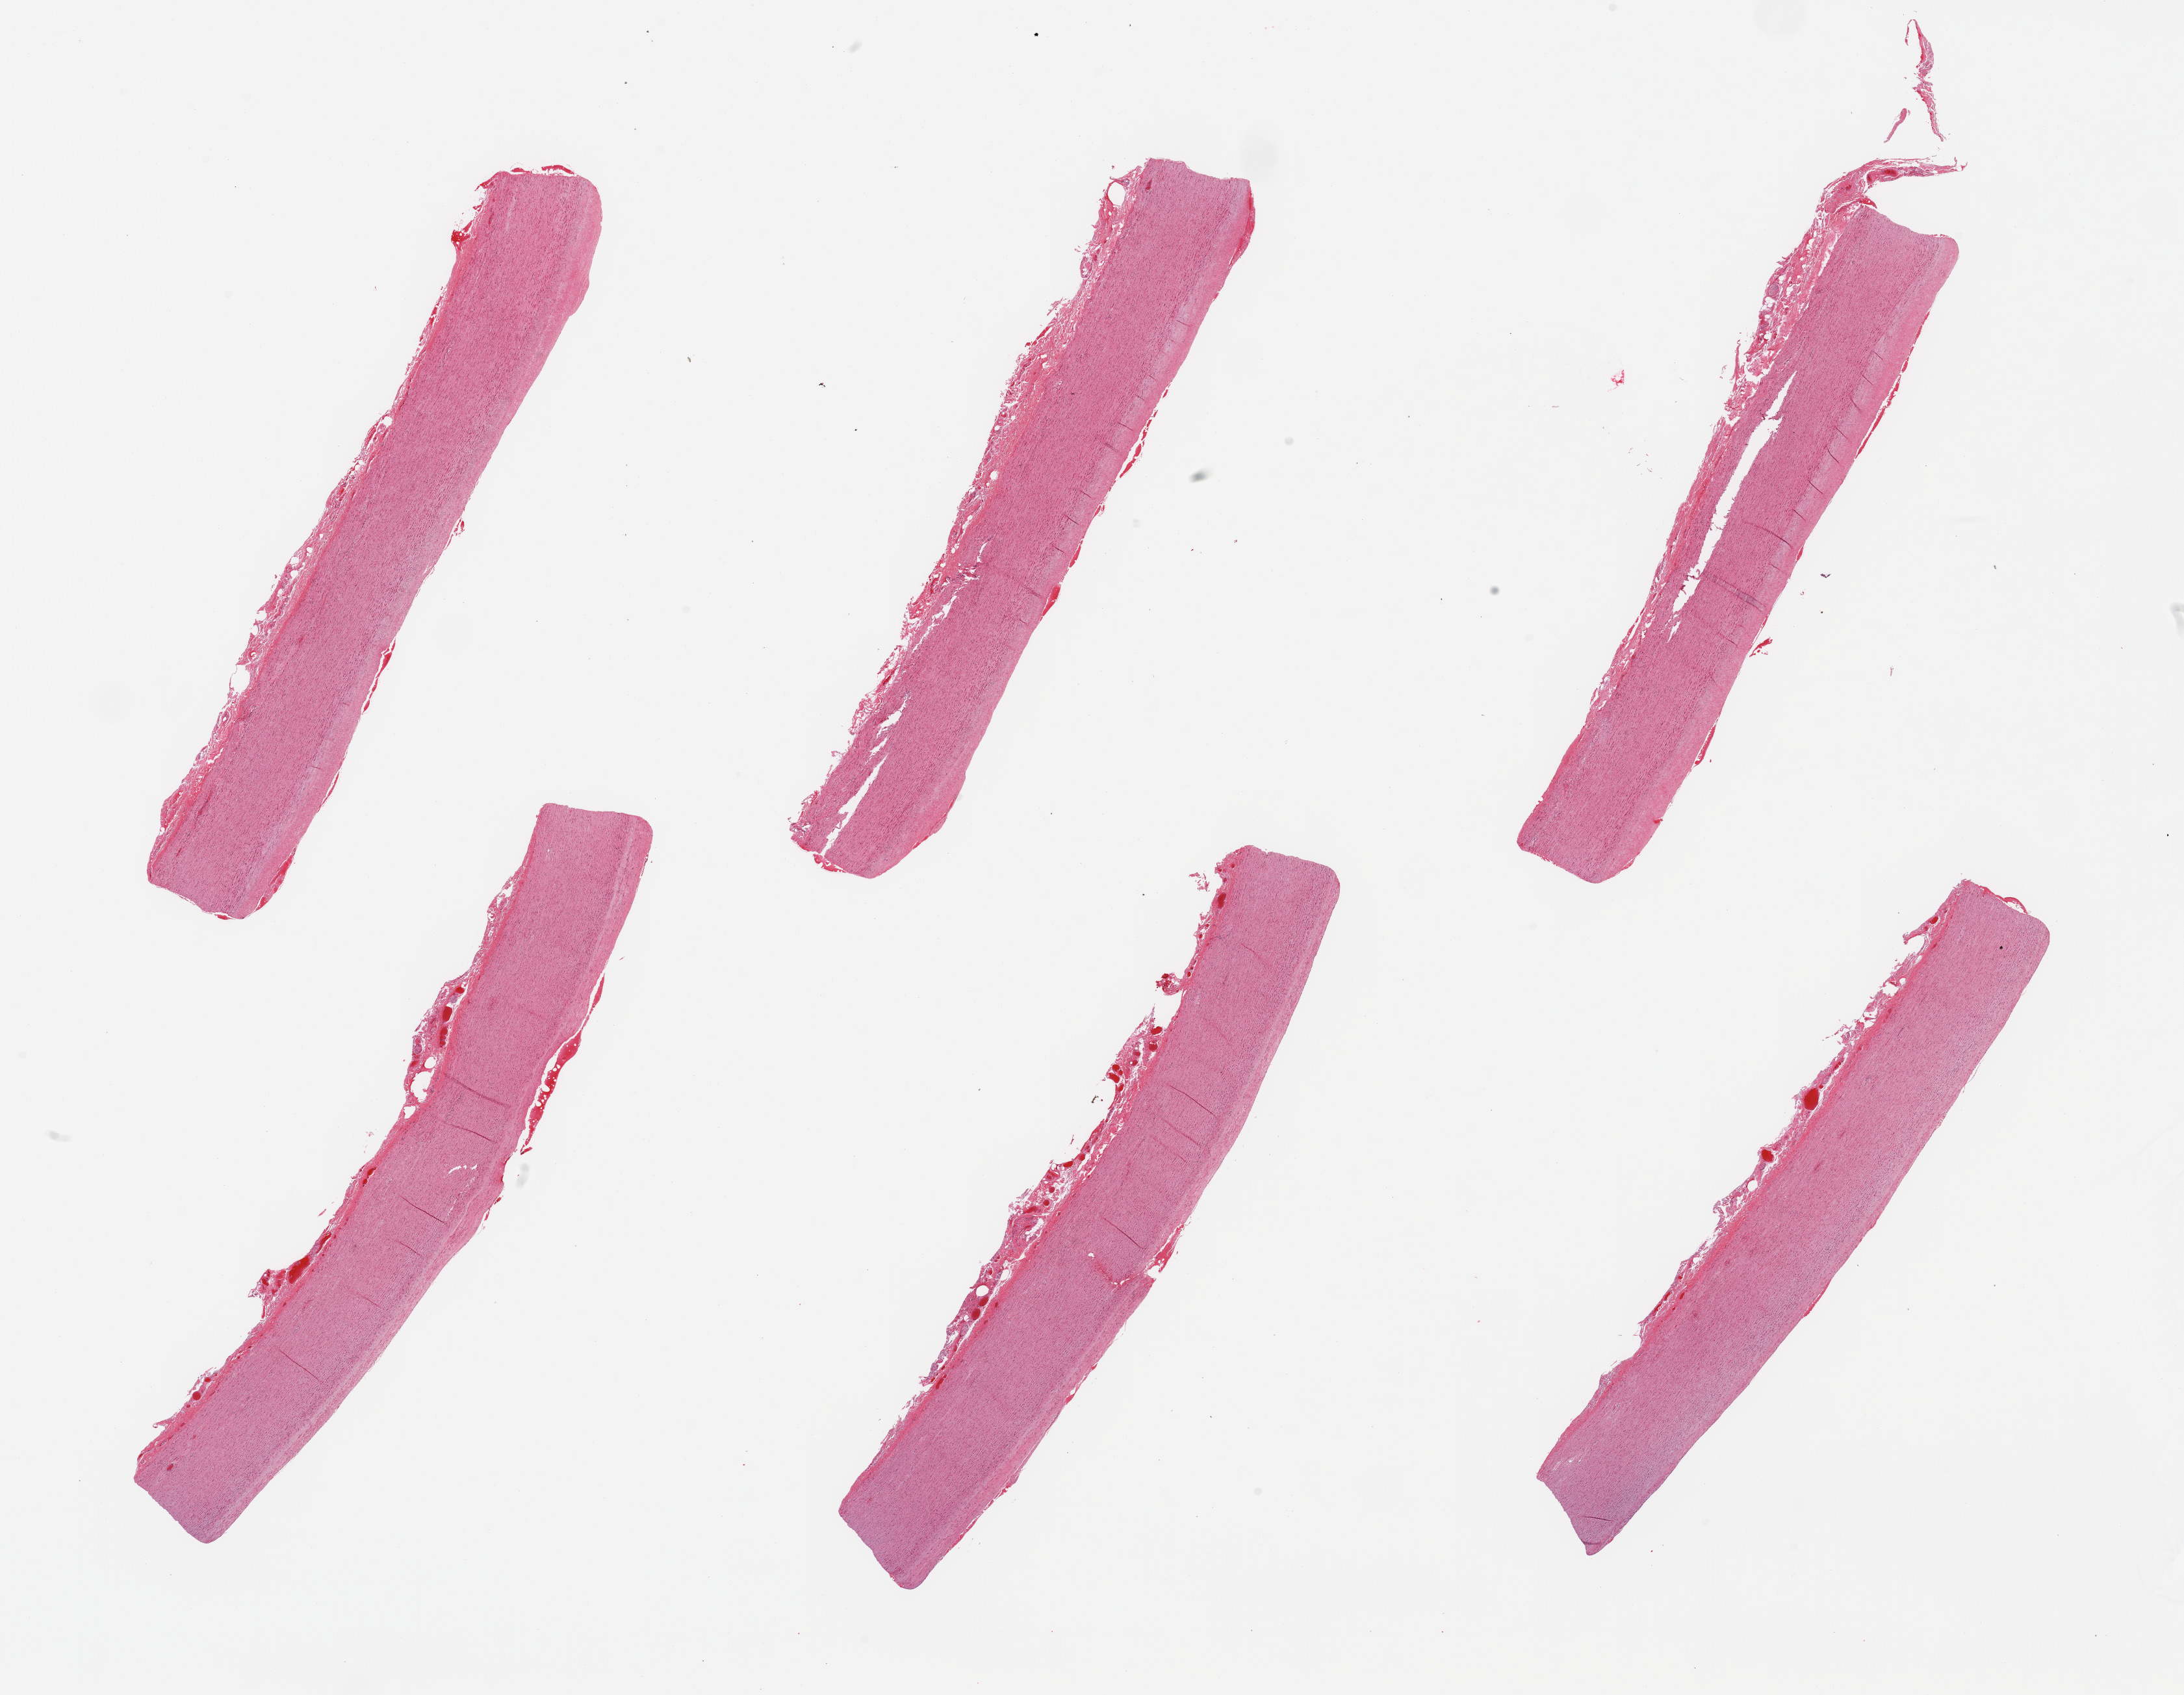
Digitized haematoxylin and eosin-stained section, whole scanned area (about 26.6 x 20.6 mm, slide scanned at 20x) shown as a low-resolution overview. PAXgene-fixed, paraffin-embedded tissue. Section of aorta (target tissue). Donor tissue sample. Male donor.
* reviewer comment on this tissue sample: 6 pieces, atherosis up to ~0.4mm